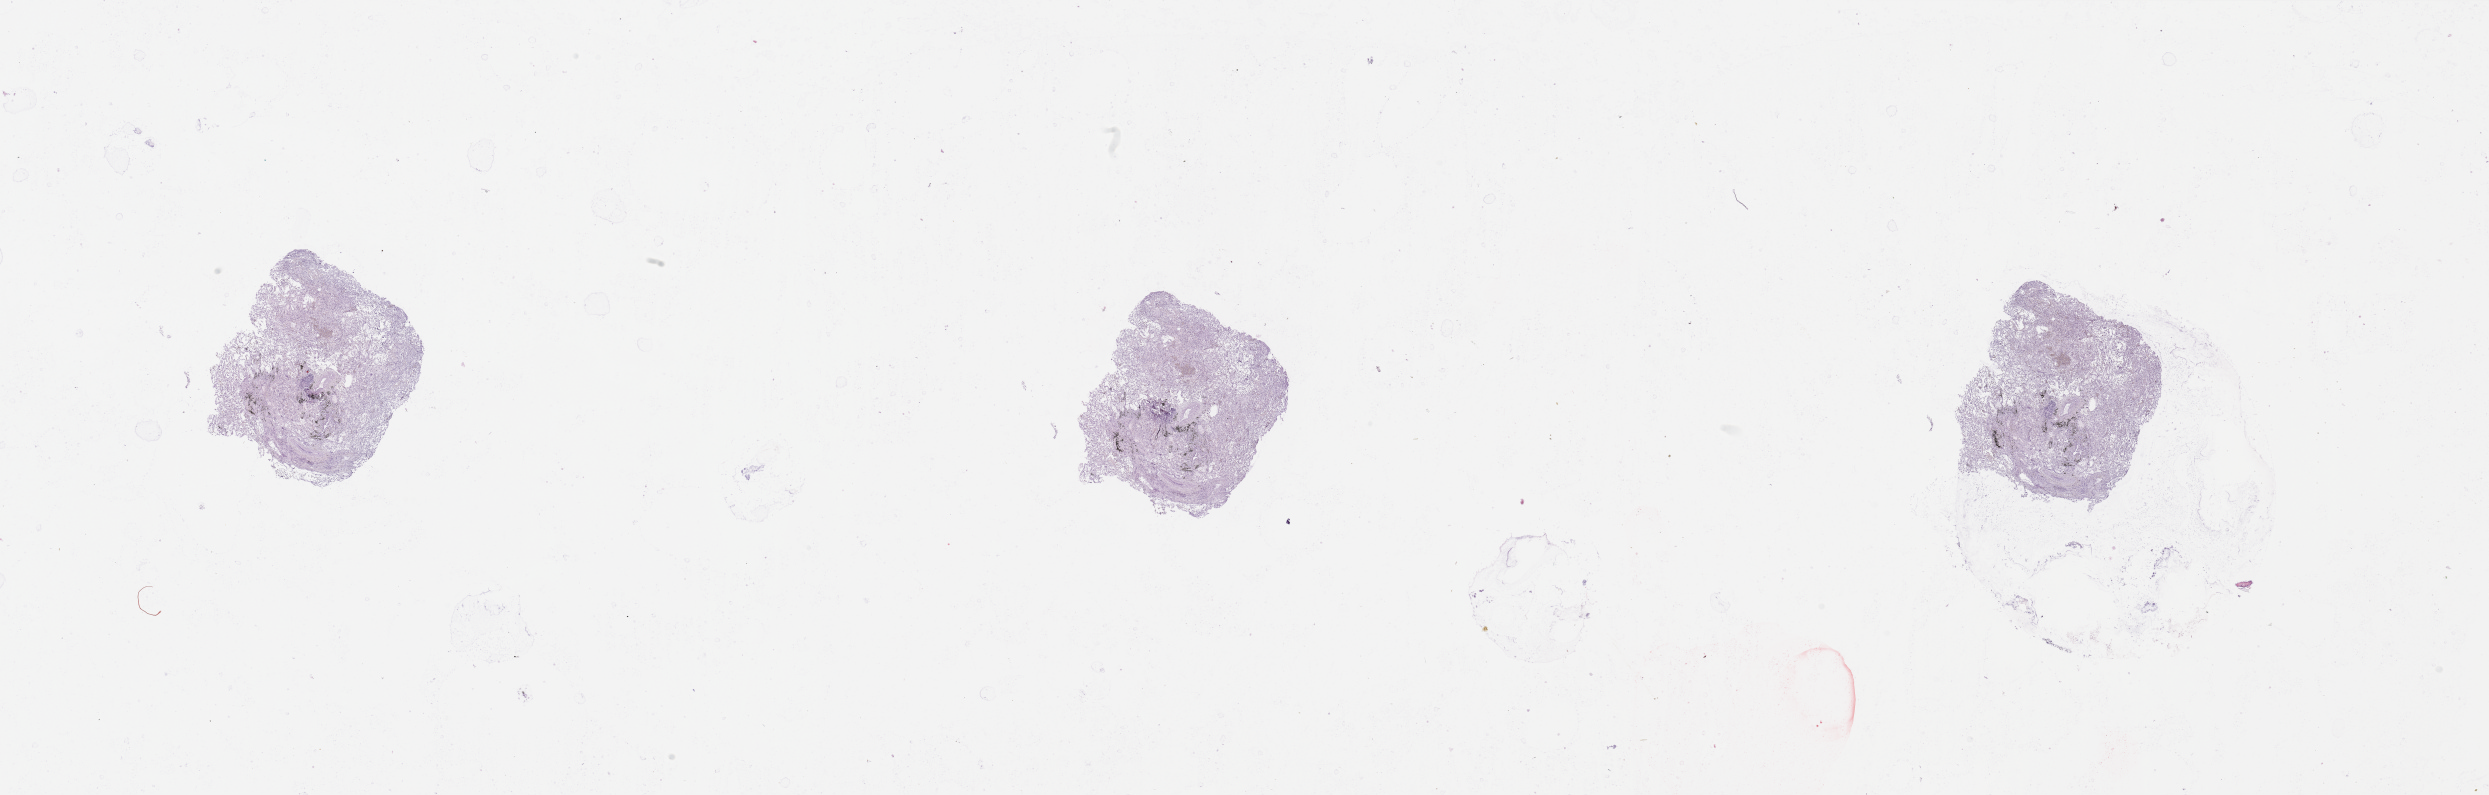
H&E whole-slide image — shown as a low-resolution overview of the whole scanned area (about 39.4 x 12.6 mm); normal (non-tumour) tissue sample, sampled site: lung. Male, 51 y/o.
• this section: normal (non-tumour) tissue from the same patient
• patient diagnosis: Squamous cell carcinoma, NOS